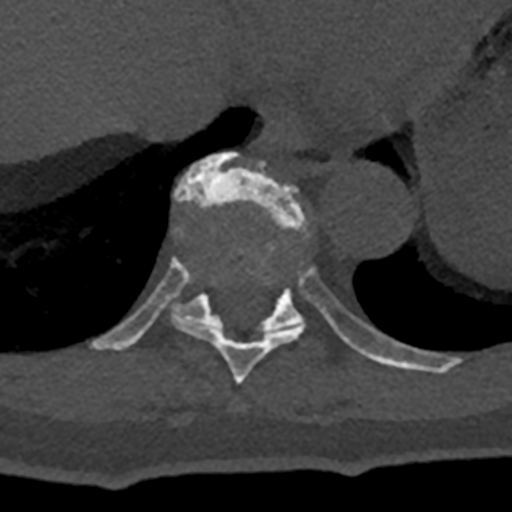
CT including the spine, one axial slice; position 632 of 797 along the scan axis; reconstruction kernel Br40s/3; 120 kVp; bone window (W 1800 / L 400 HU); 0.5 mm slice thickness; 512 × 512 image matrix, field of view 160 × 160 mm. Male patient, age 74 years. From the clinical record (not read from this slice): primary cancer: renal; vertebrae with lytic lesions (as recorded): T10, L1, L2, L3, L4, L5.
Structures marked on this image (semi-automatically segmented with operator editing):
- T10 vertebra: bounding box (x1, y1, x2, y2) in pixels: (91, 151, 432, 372)
- T9 vertebra: (172, 257, 305, 384)